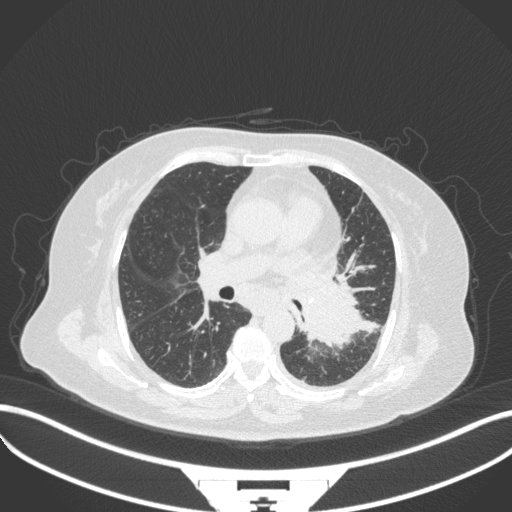
Chest CT, one axial slice. Slice 190 of 328 in the series (ordered by position). Reconstruction kernel B31f. Lung window (W 1500 / L -600 HU). 1 mm slice thickness. 512 × 512 image matrix. Patient: female, 69 years. From the clinical record (not read from this slice): clinical TNM (as recorded): T2b N3 M1.
Outlined on this slice (rectangle marked by the reading radiologist):
- lung tumour (recorded histology: adenocarcinoma): bounding box <302,277,364,349> (left, top, right, bottom; pixels)